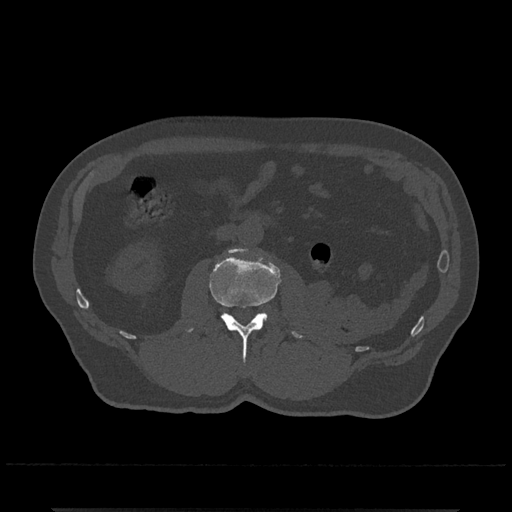
CT including the spine, one axial slice. Position 283 of 797 along the scan axis. Reconstruction kernel Br40s/3. 120 kVp. Bone window (W 1800 / L 400 HU). 512 × 512 image matrix, field of view 393 × 393 mm. Patient: male, 67 years. Case-level facts recorded for this patient, not image findings: primary cancer: prostate.
Annotated regions visible in this slice (semi-automatically segmented with operator editing):
- L2 vertebra: bounding box [x1, y1, x2, y2] px = [187, 247, 302, 361]
- L3 vertebra: [260, 312, 265, 315]